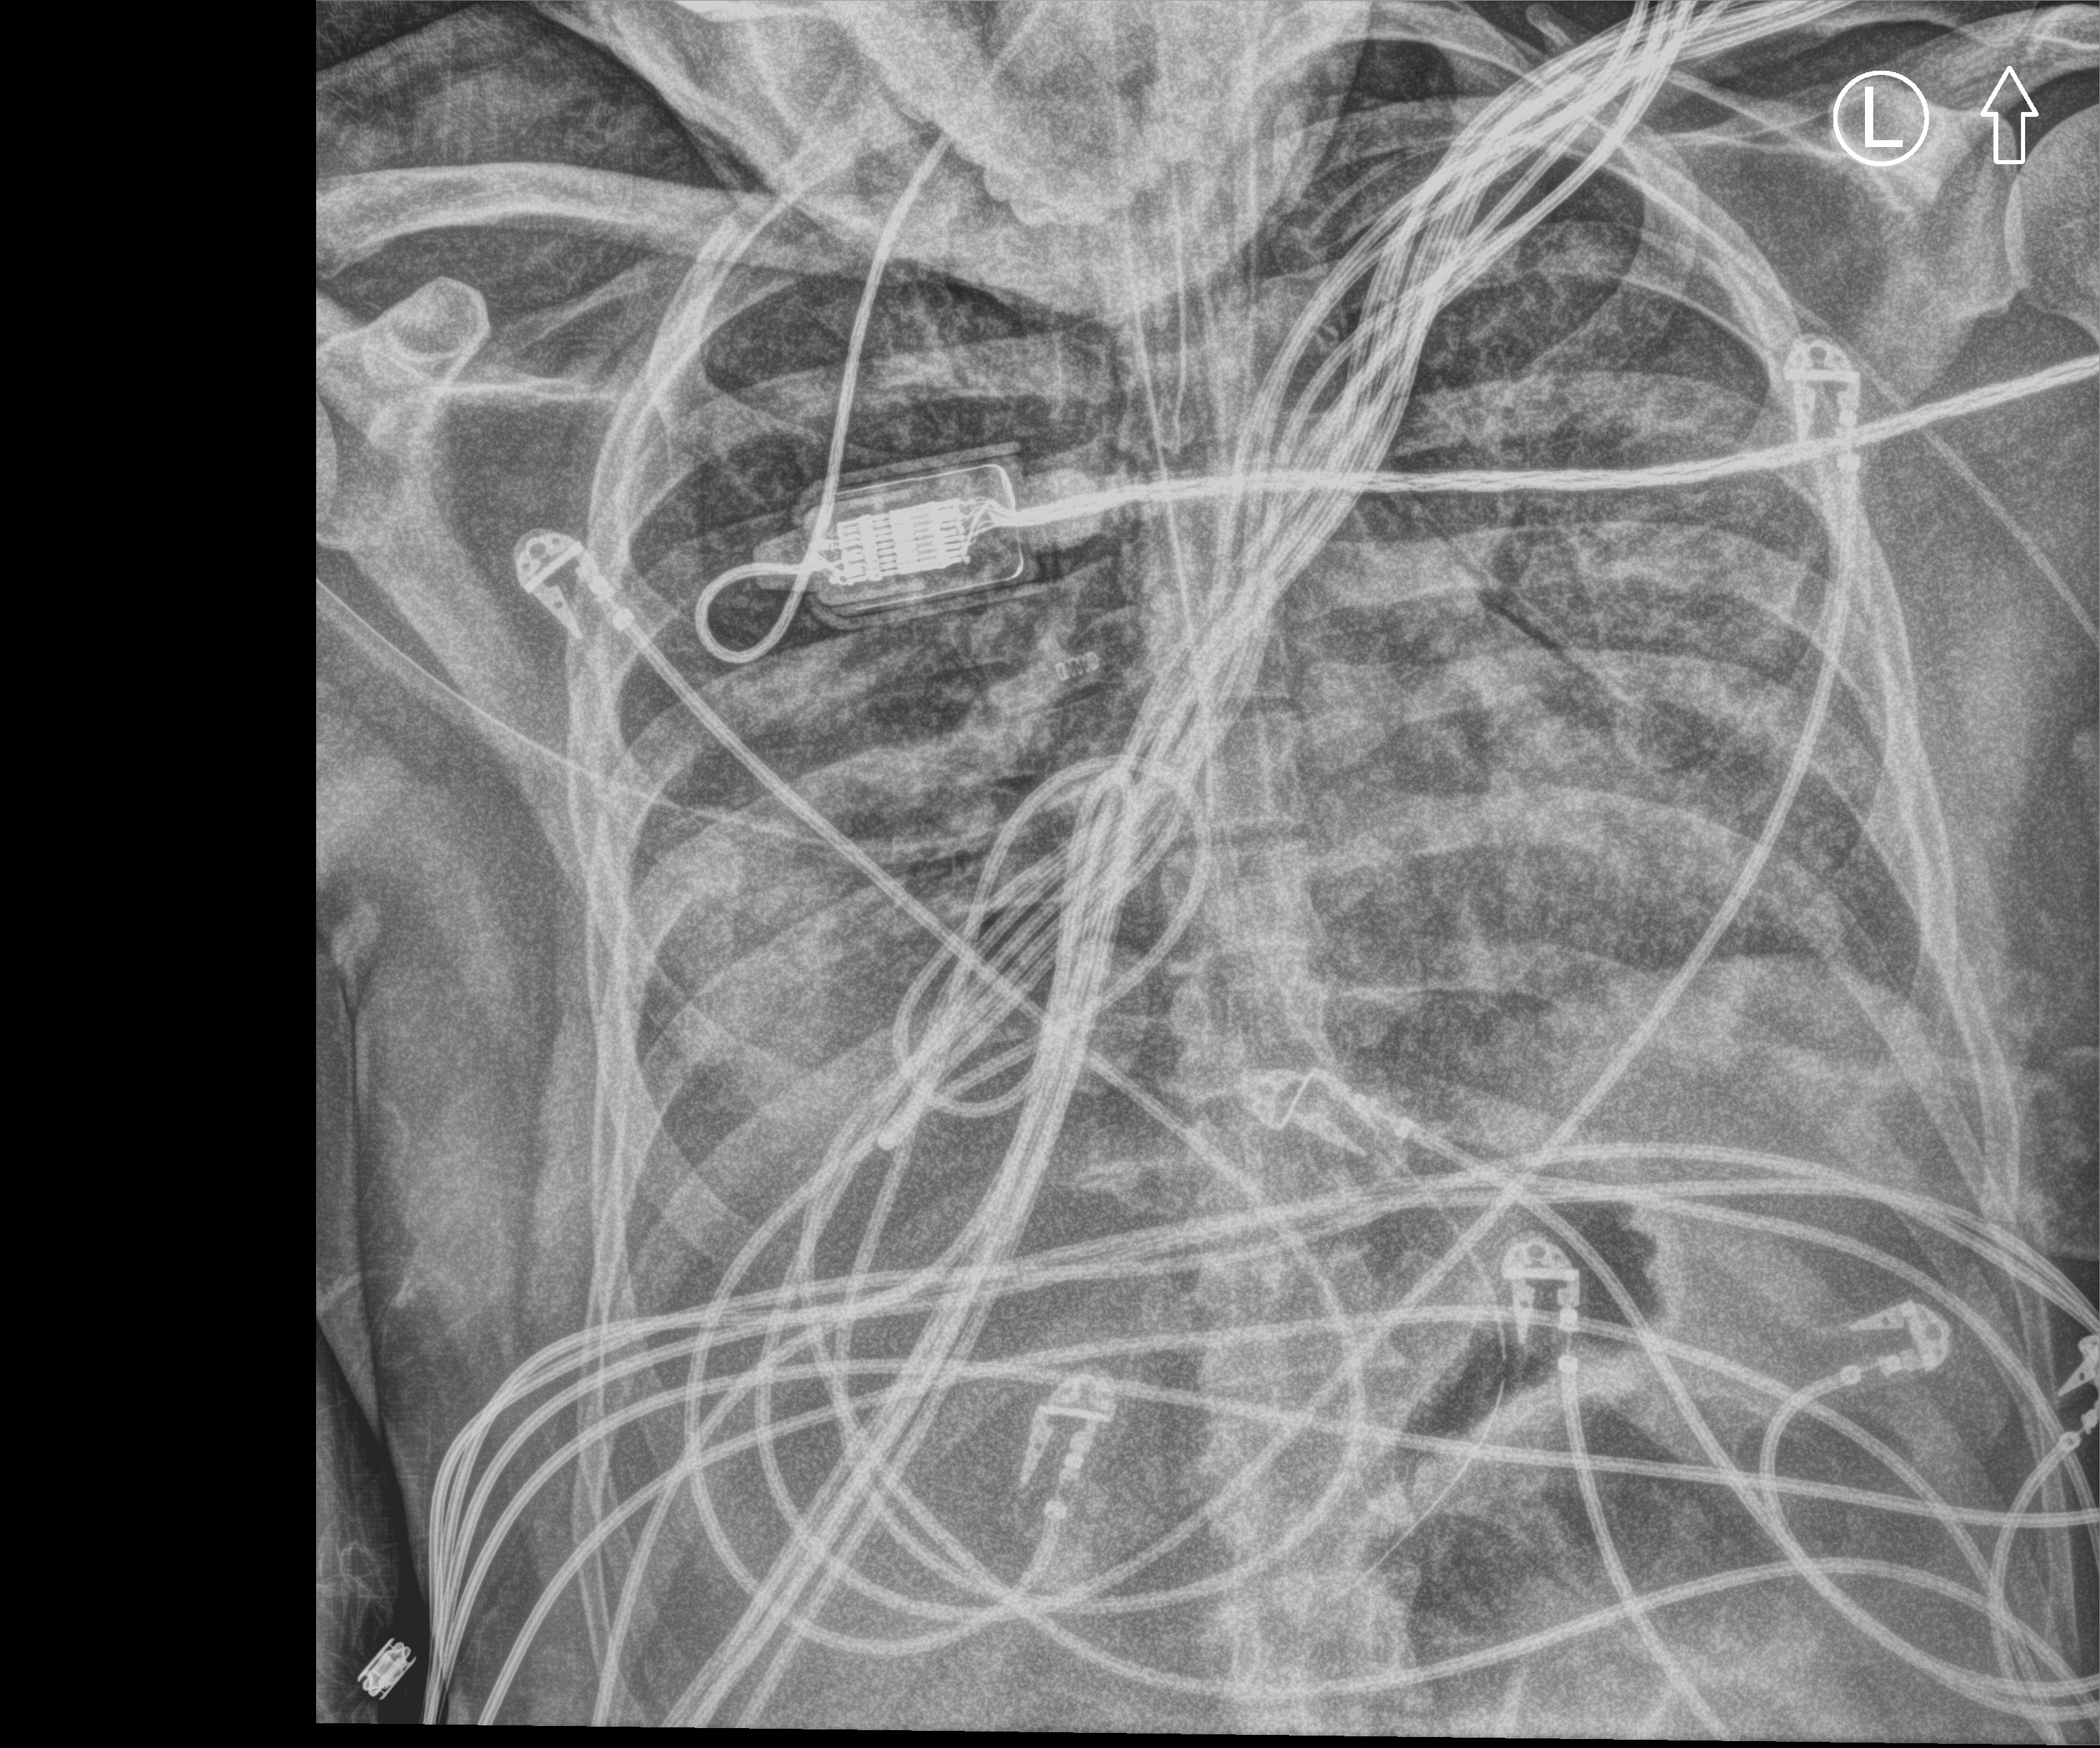
Chest X-ray (portable), anteroposterior (AP) projection. Male patient hospitalised with COVID-19, age 18–59 years.
From the hospital-stay record, not from the radiograph (when in the stay this image was taken is not recorded): COPD (admission record): no.